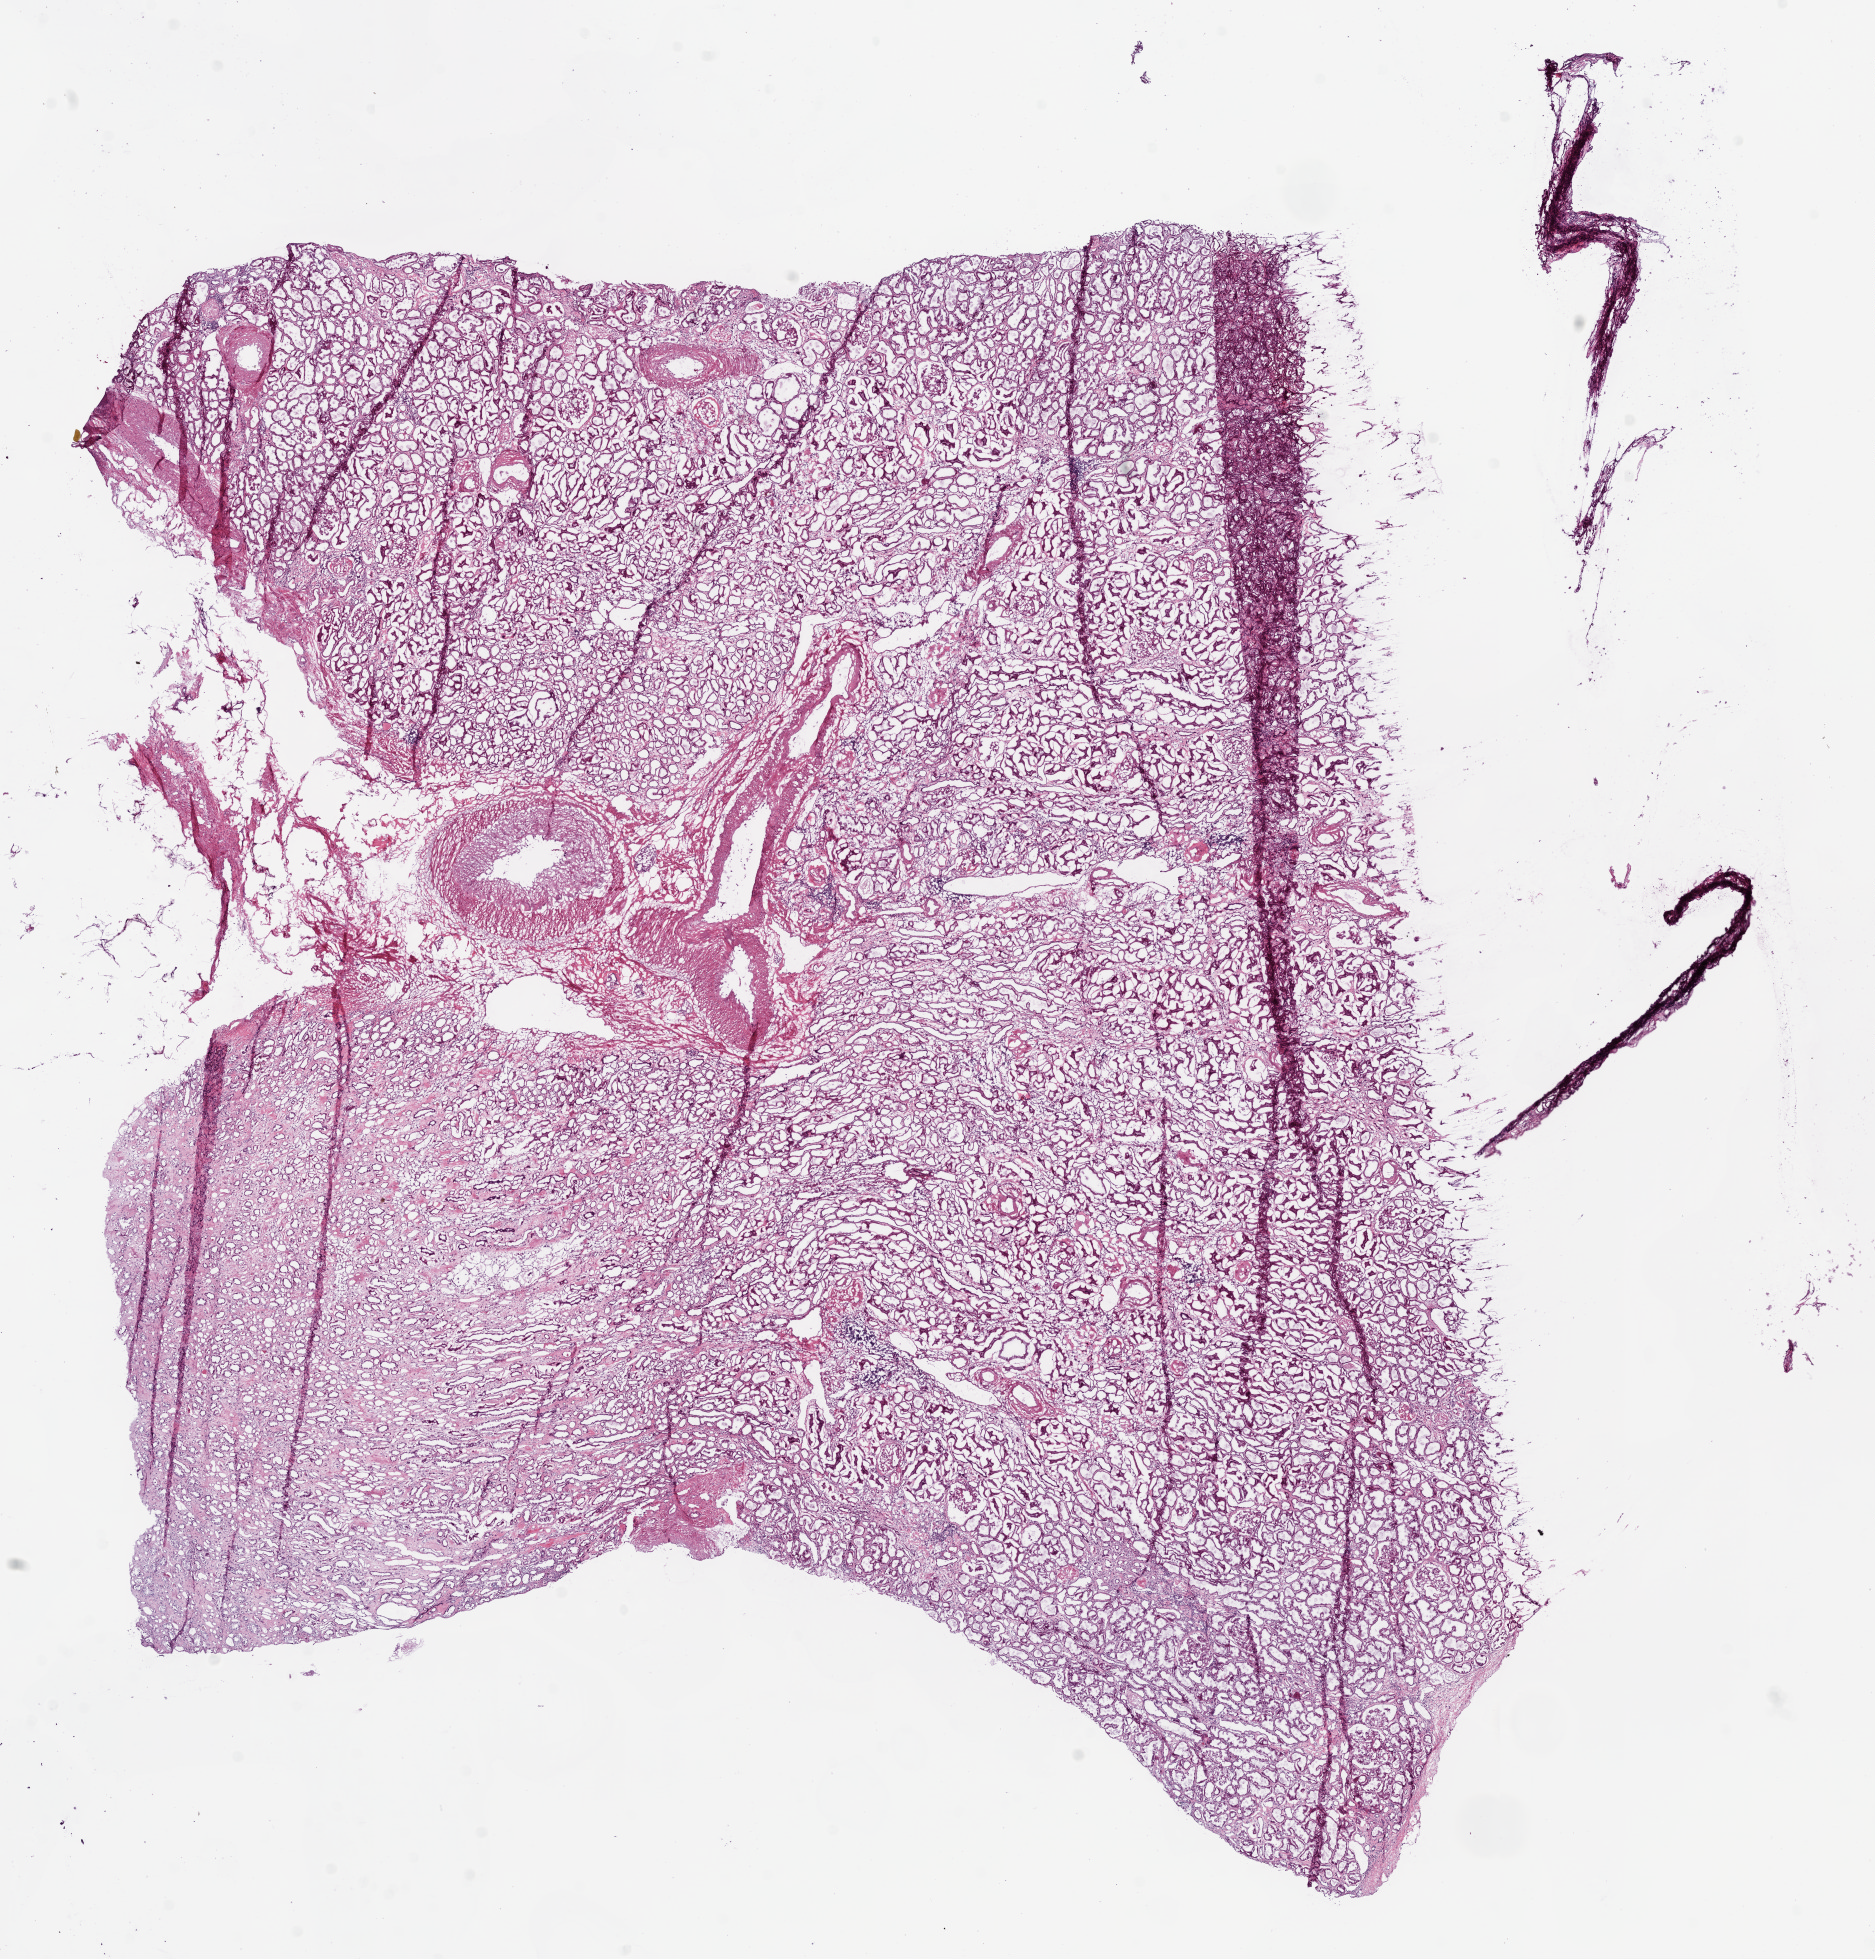
Digitized H&E tissue section (whole slide), low-resolution overview of the scanned area, about 15.0 x 15.7 mm (from a 20x scan), frozen section from the bottom of the tissue portion, kidney, solid tissue normal (non-tumour tissue) sample. Male patient; age at initial diagnosis 79 years.
* this section: solid tissue normal sample (biorepository sample class)
* patient diagnosis: Clear cell adenocarcinoma, NOS